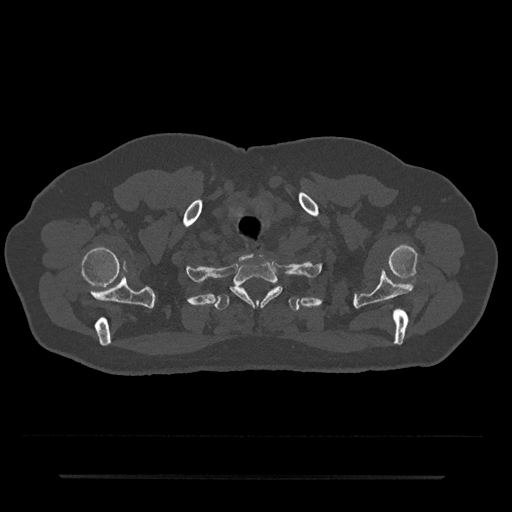
CT including the spine, one axial slice; reconstruction kernel Br40s/3; bone window (W 1800 / L 400 HU); 0.5 mm slice thickness; 512 × 512 image matrix. Male patient, age 69 years. Case-level facts recorded for this patient, not image findings: primary cancer: prostate.
Structures marked on this image (semi-automatically segmented with operator editing):
- T1 vertebra: bounding box <231,261,282,306> (left, top, right, bottom; pixels)
- T2 vertebra: <215,287,300,312>